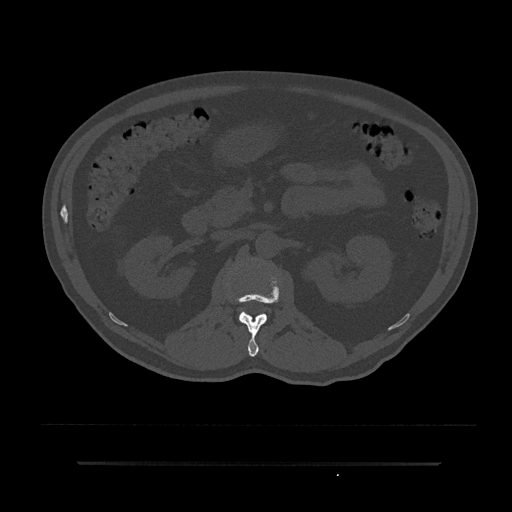
CT including the spine, one axial slice. Position 120 of 797 along the scan axis. Reconstruction kernel Br40s/3. Bone window (W 1800 / L 400 HU). 0.5 mm slice thickness. 512 × 512 image matrix. Patient: male, 59 years. From the clinical record (not read from this slice): primary cancer: bile ducts; vertebrae with lytic lesions (as recorded): T10.
Structures marked on this image (semi-automatic segmentation, software-assisted and operator-edited):
- L1 vertebra: bounding box [x1, y1, x2, y2] px = [234, 273, 281, 357]
- L2 vertebra: [240, 312, 242, 314]